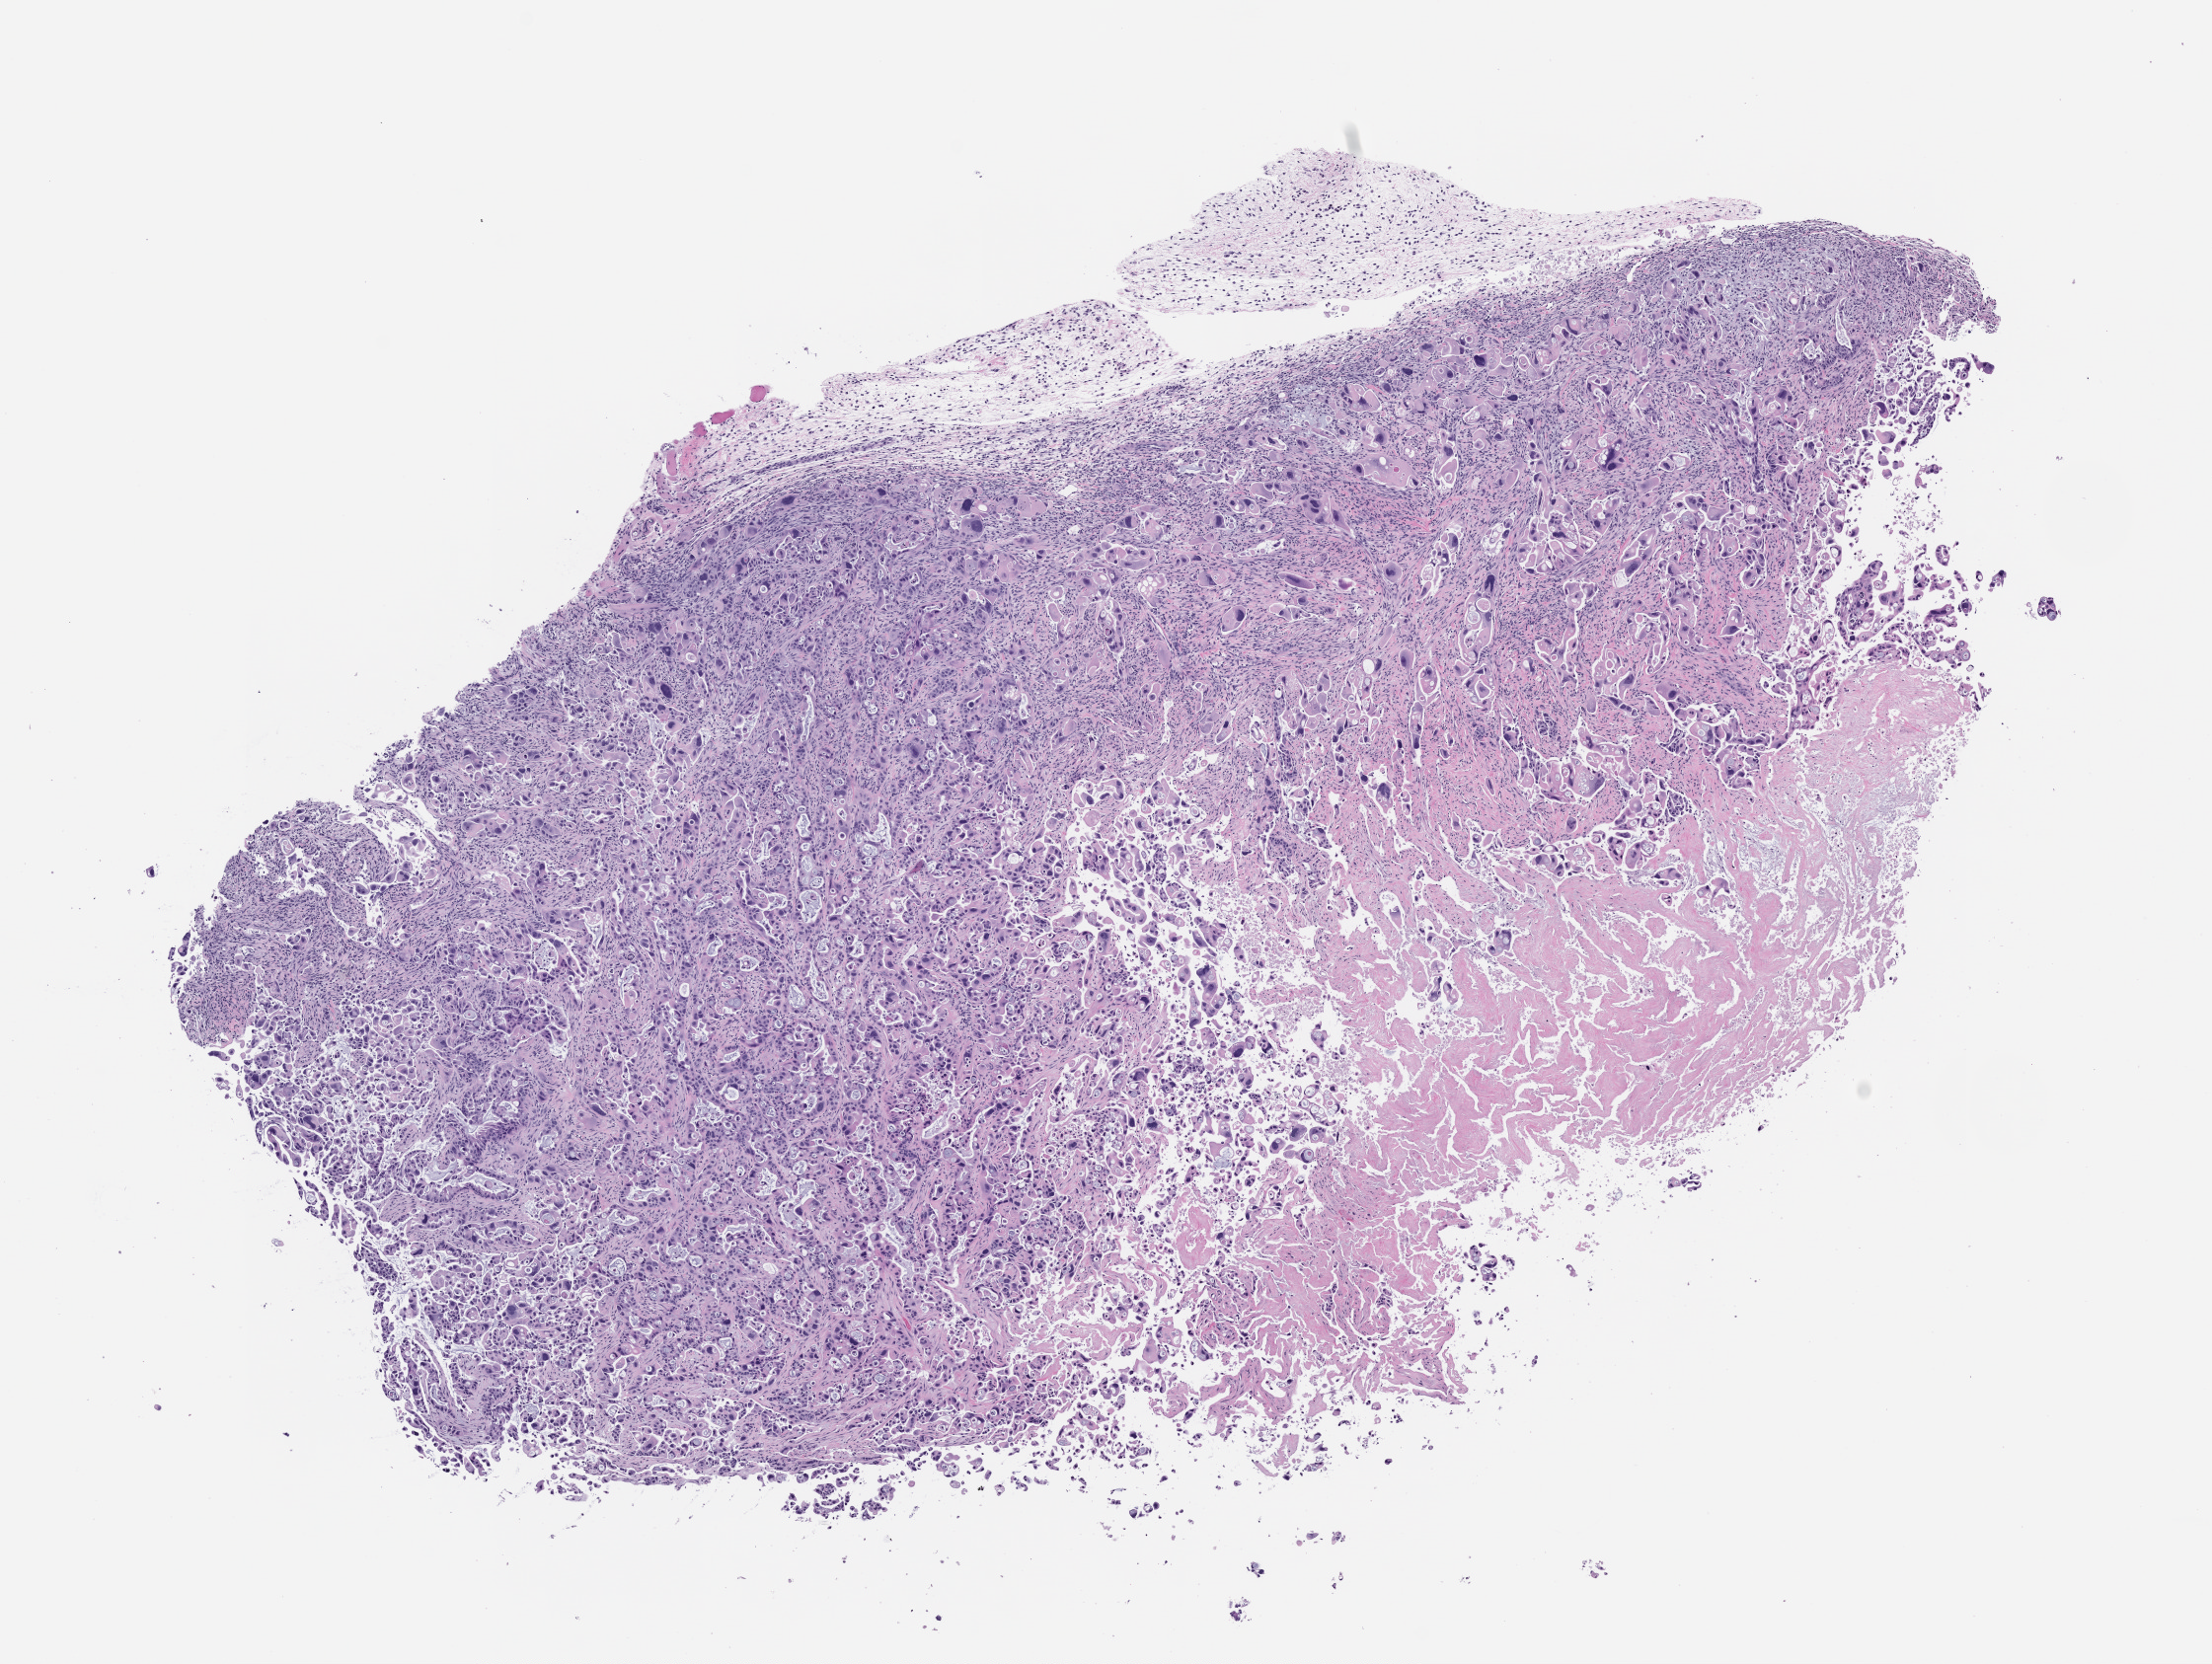
Hematoxylin and eosin (H&E) whole-slide image of a patient-derived xenograft (PDX) tumor grown in a mouse, passage 0 — a low-resolution overview of the entire scanned area, about 9.0 x 6.8 mm, formalin-fixed paraffin-embedded section, tumor site category: pancreas.
• originating patient diagnosis: Pancreatic Adenocarcinoma